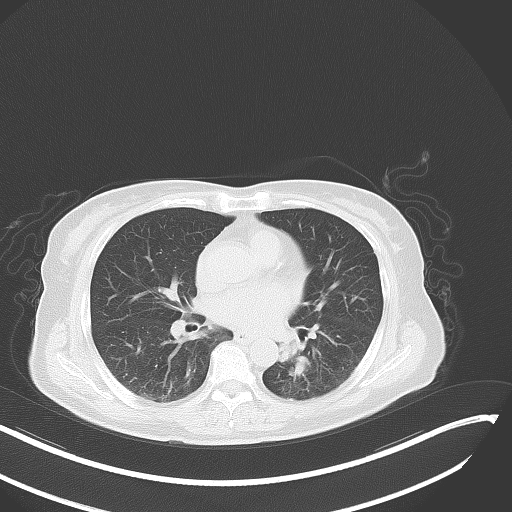
Chest CT, one axial slice; position 18 of 48 along the scan axis; reconstruction kernel B70f; 120 kVp; lung window (W 1500 / L -600 HU); 5 mm slice thickness; 512 × 512 image matrix, field of view 400 × 400 mm. Patient: female, 64 years. Case-level facts recorded for this patient, not image findings: clinical TNM (as recorded): T3 N1 M1; histopathological grade: G3.
Annotated regions visible in this slice (bounding box drawn by a radiologist):
- lung tumour (recorded histology: small cell carcinoma): bounding box <279,328,310,377> (left, top, right, bottom; pixels)